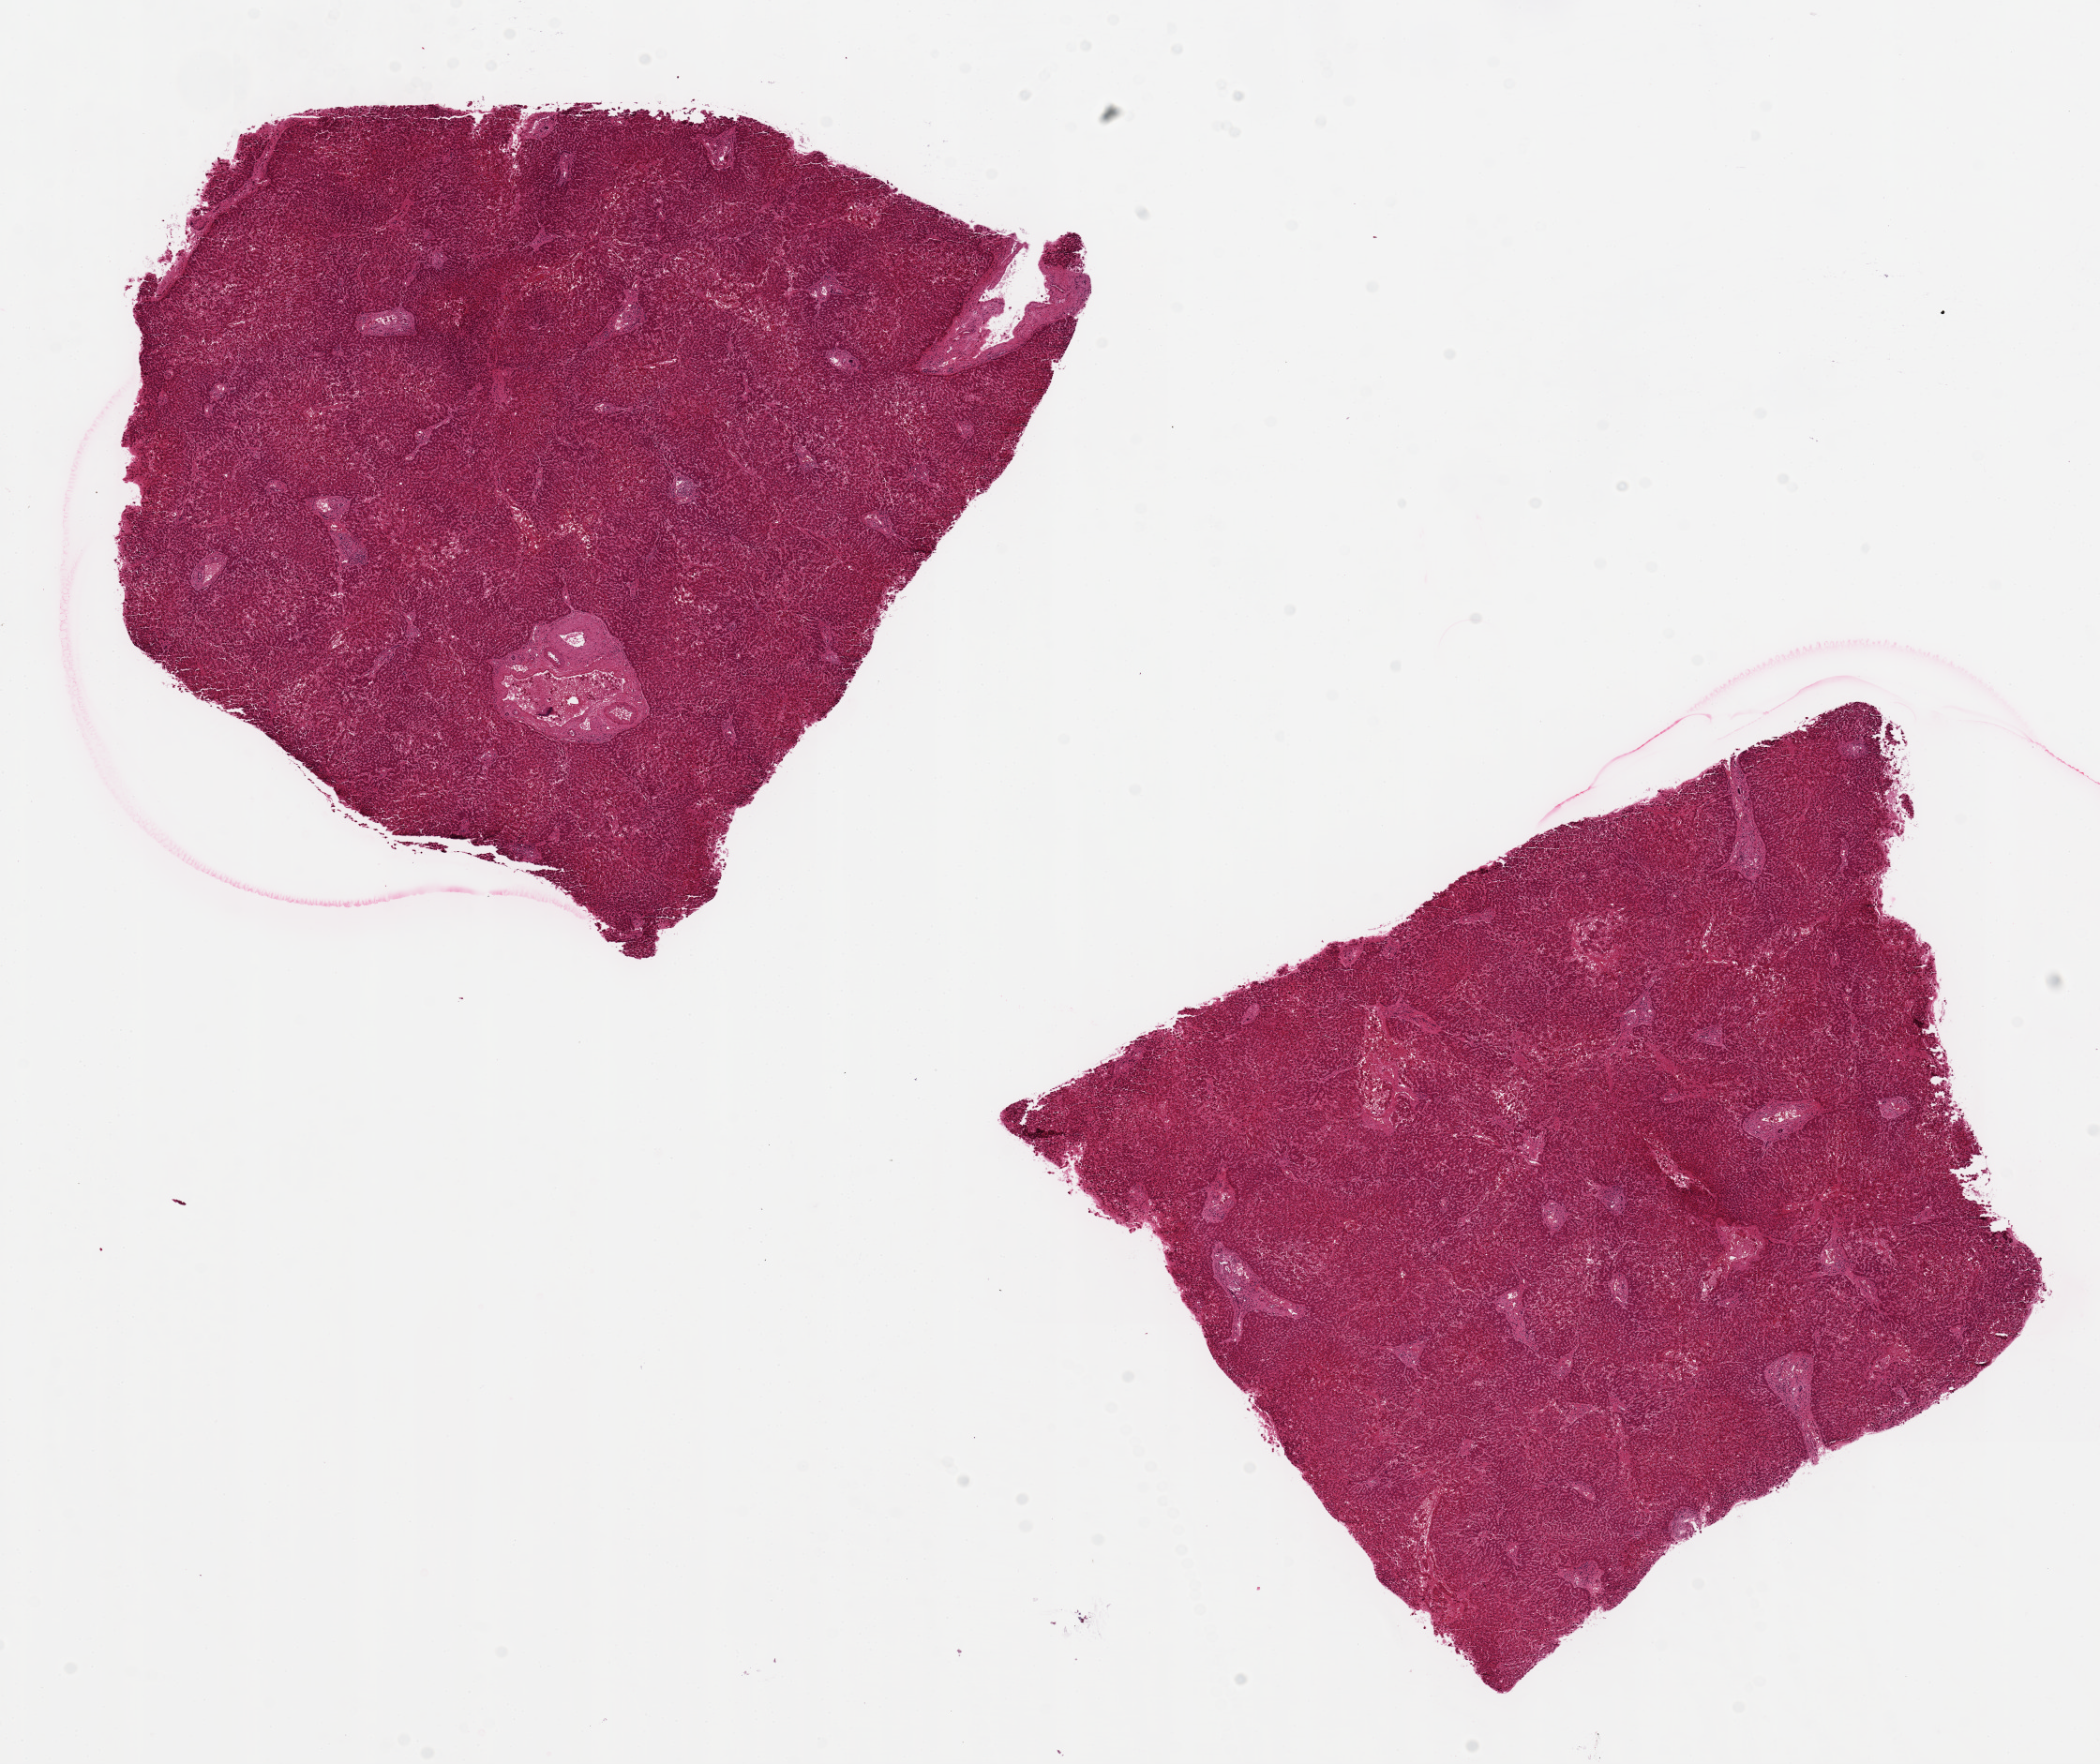
Digitized H&E-stained section, brightfield, whole scanned area (about 17.7 x 14.9 mm) shown as a low-resolution overview, PAXgene-fixed paraffin-embedded (PFPE) section, target tissue: liver, tissue donor sample. Donor: male.
- pathologist's review note for this sample: 2 aliquots, ~7x7mm